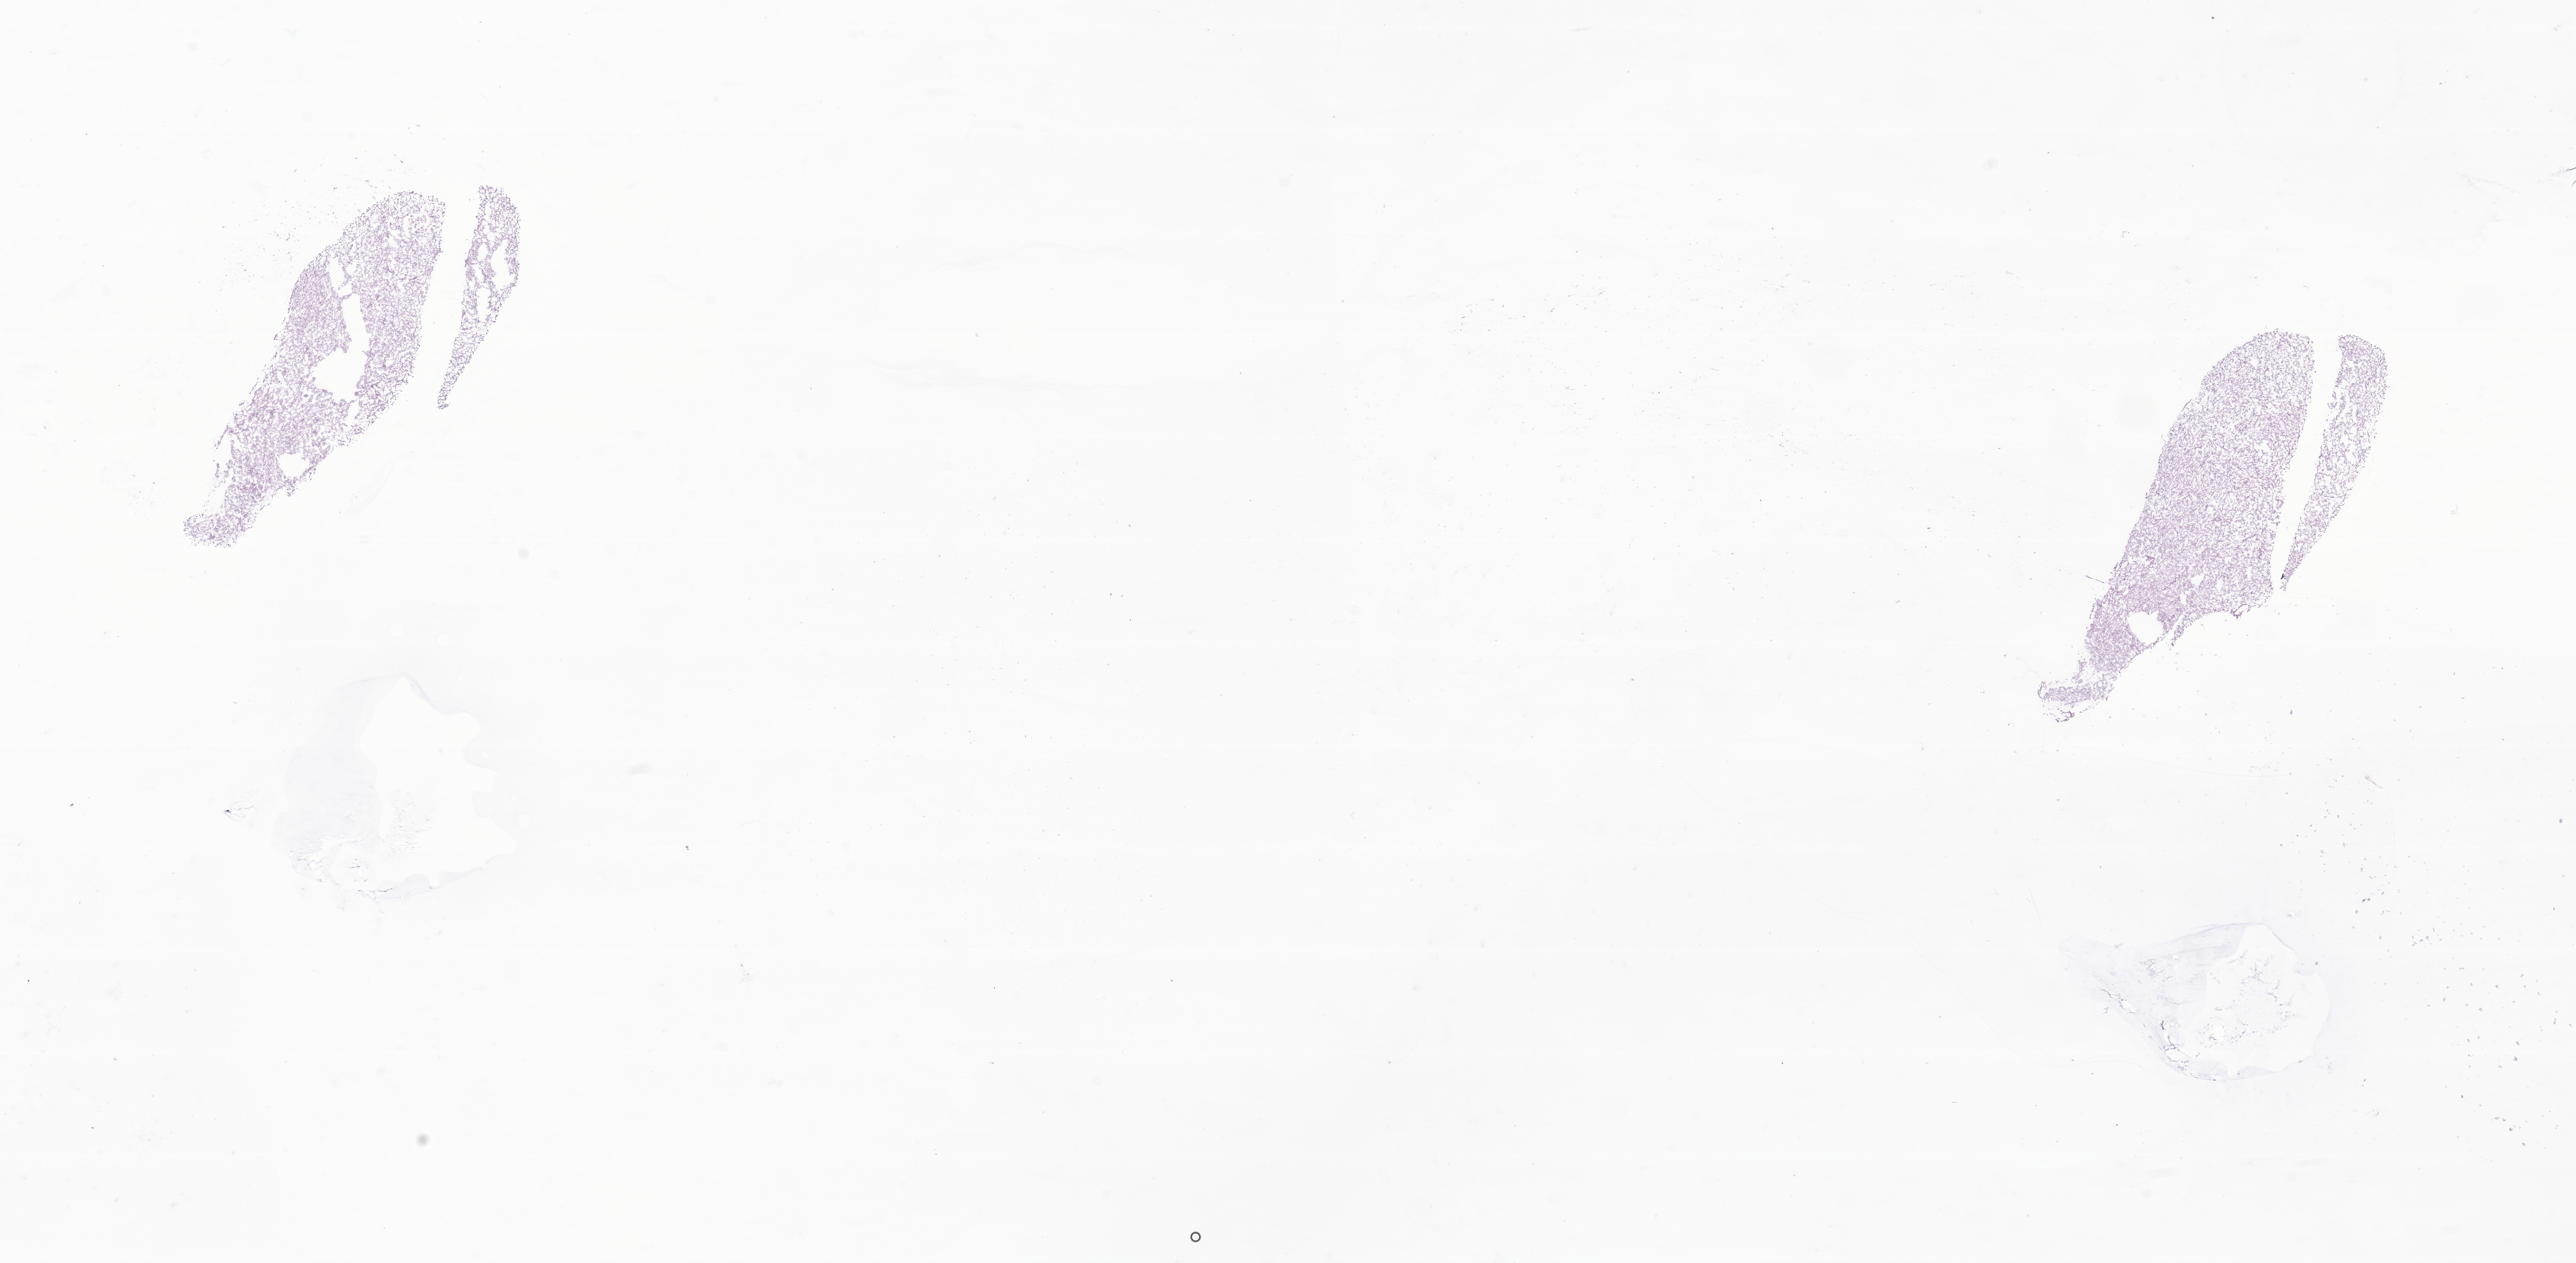
Digitized H&E-stained section of tumor tissue from the cerebellum, a low-resolution overview of the entire scanned area, about 26.8 x 13.1 mm, frozen section (OCT-embedded). Patient: male, age 66 months (5 years 6 months).
Diagnosis: Pilocytic astrocytoma.